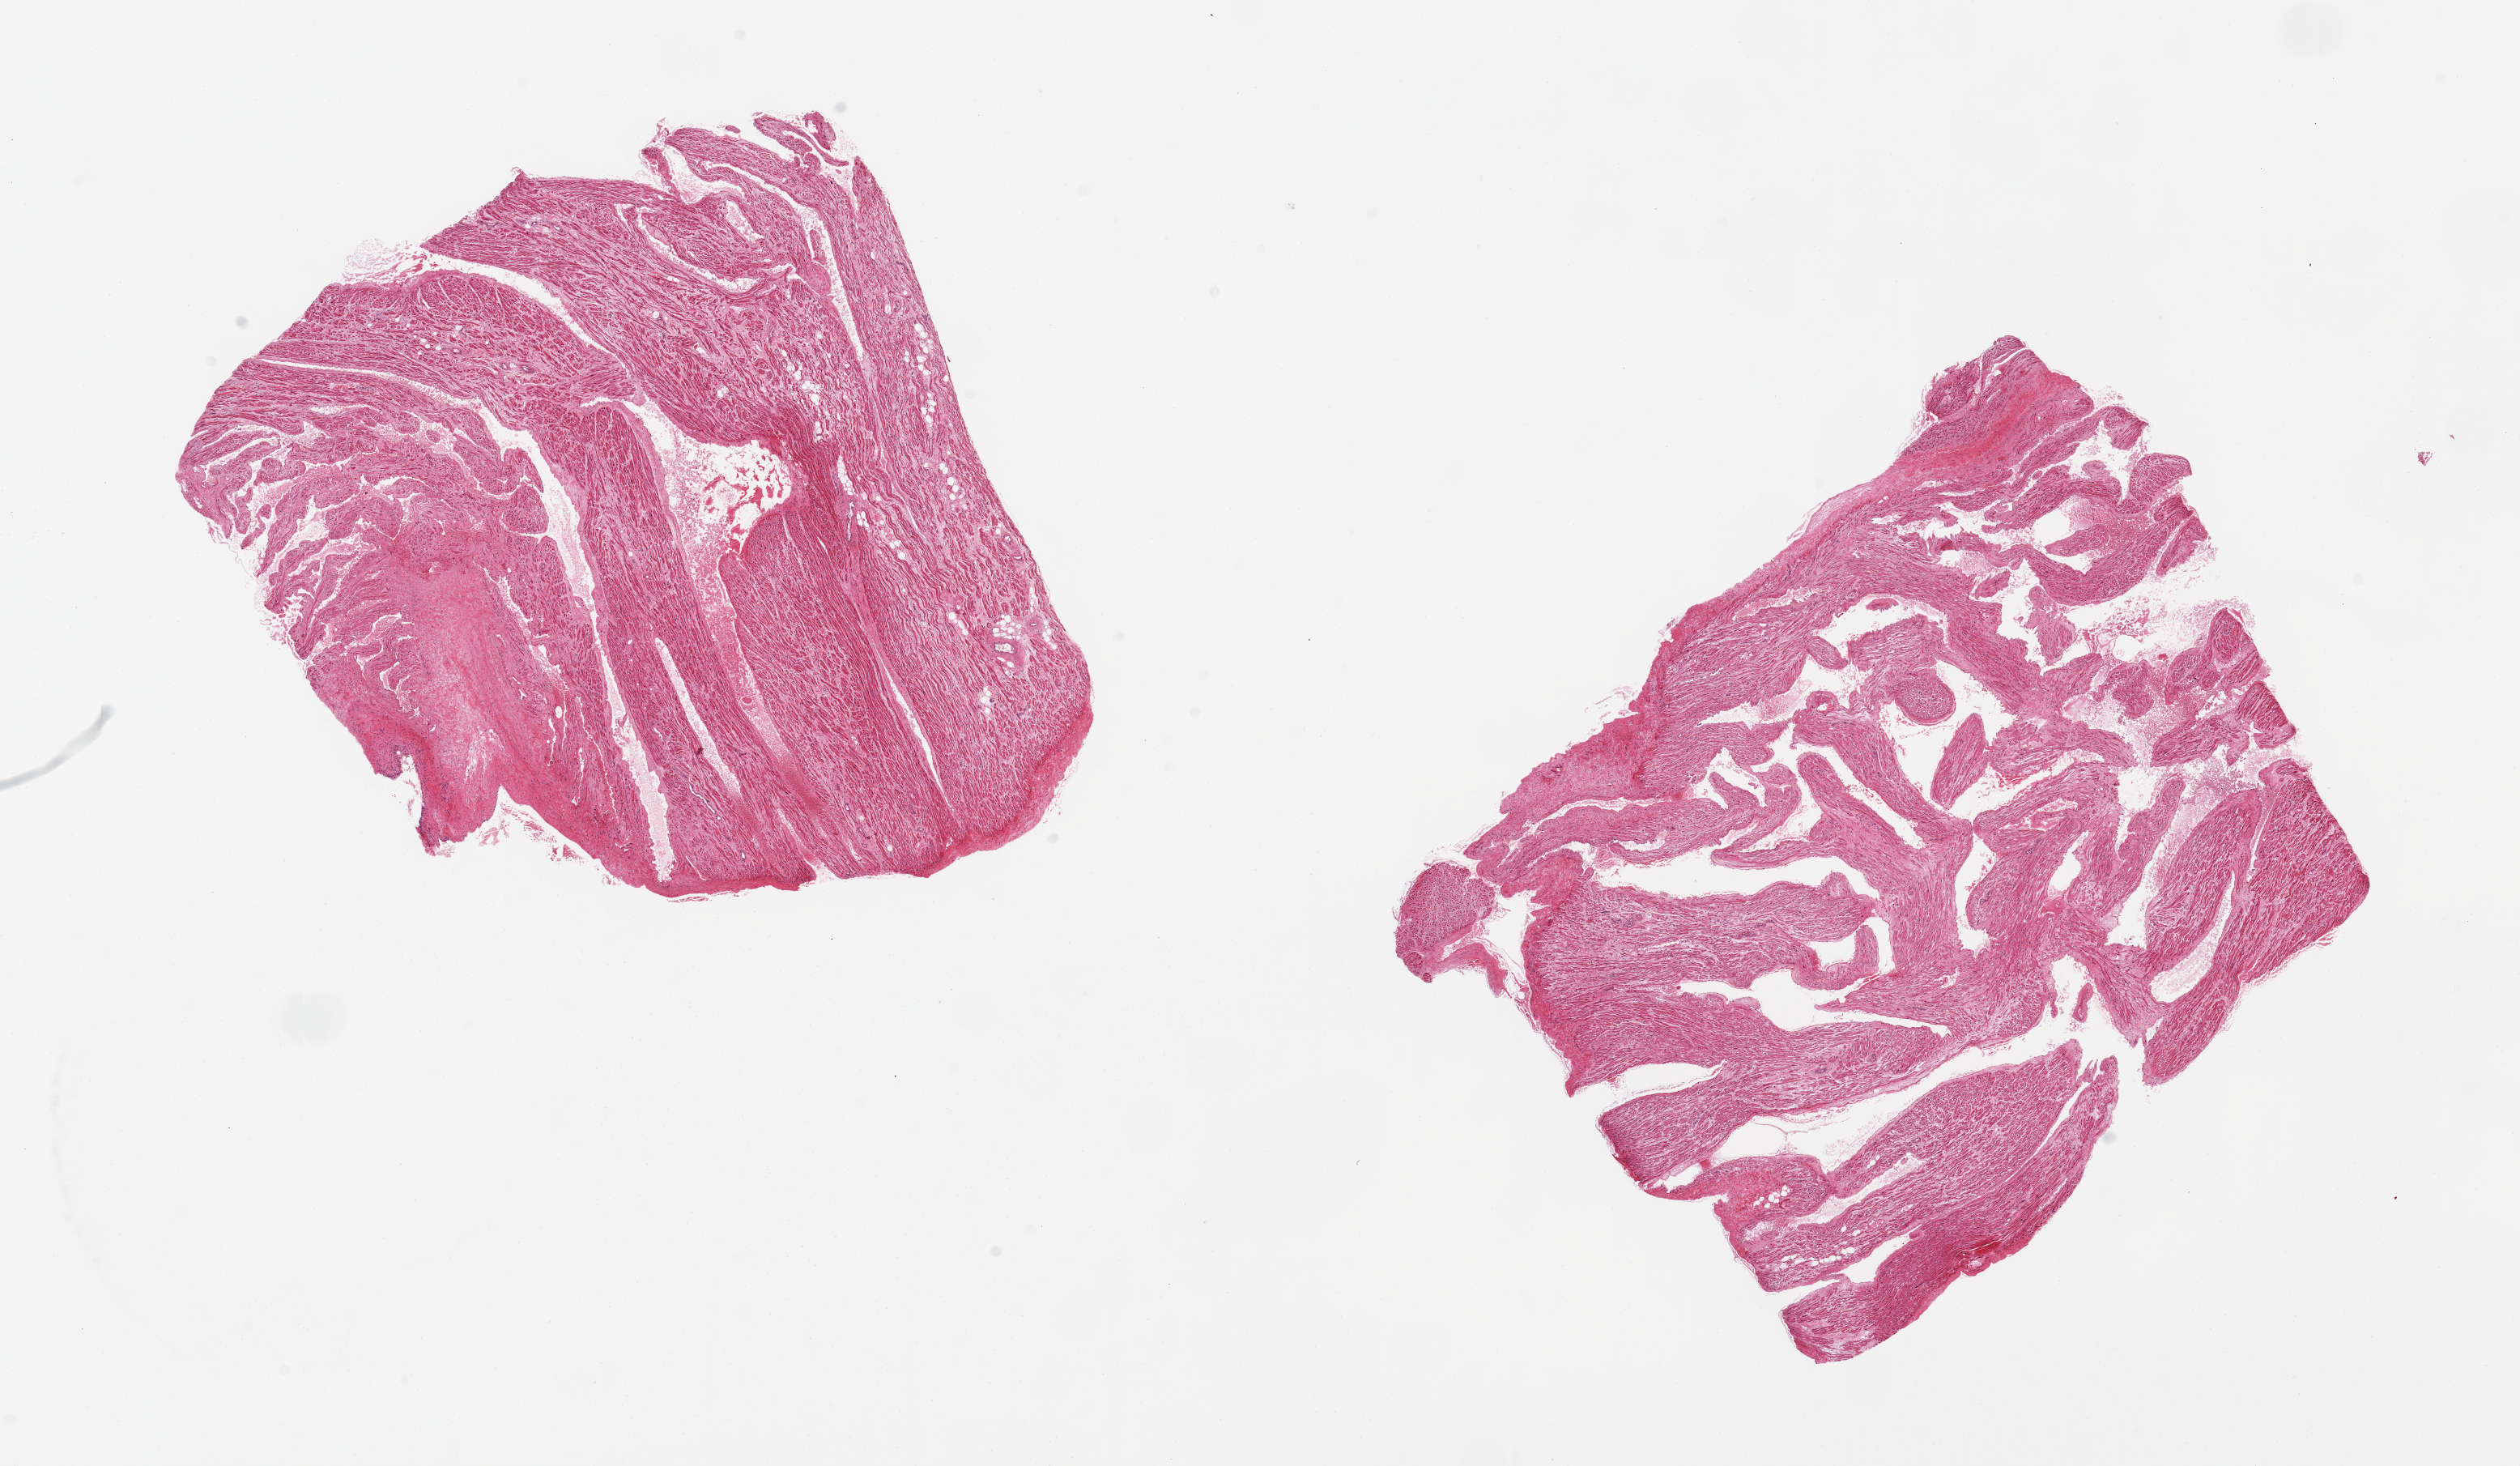
Digitized hematoxylin and eosin (H&E)-stained section, brightfield, low-resolution overview of the scanned area, about 24.6 x 14.3 mm; PAXgene-fixed, paraffin-embedded tissue; sampled site (target tissue): auricular appendage; donor tissue sample.
Pathologist's review note for this sample: 2 pieces. 8x7 & 9x7mm.